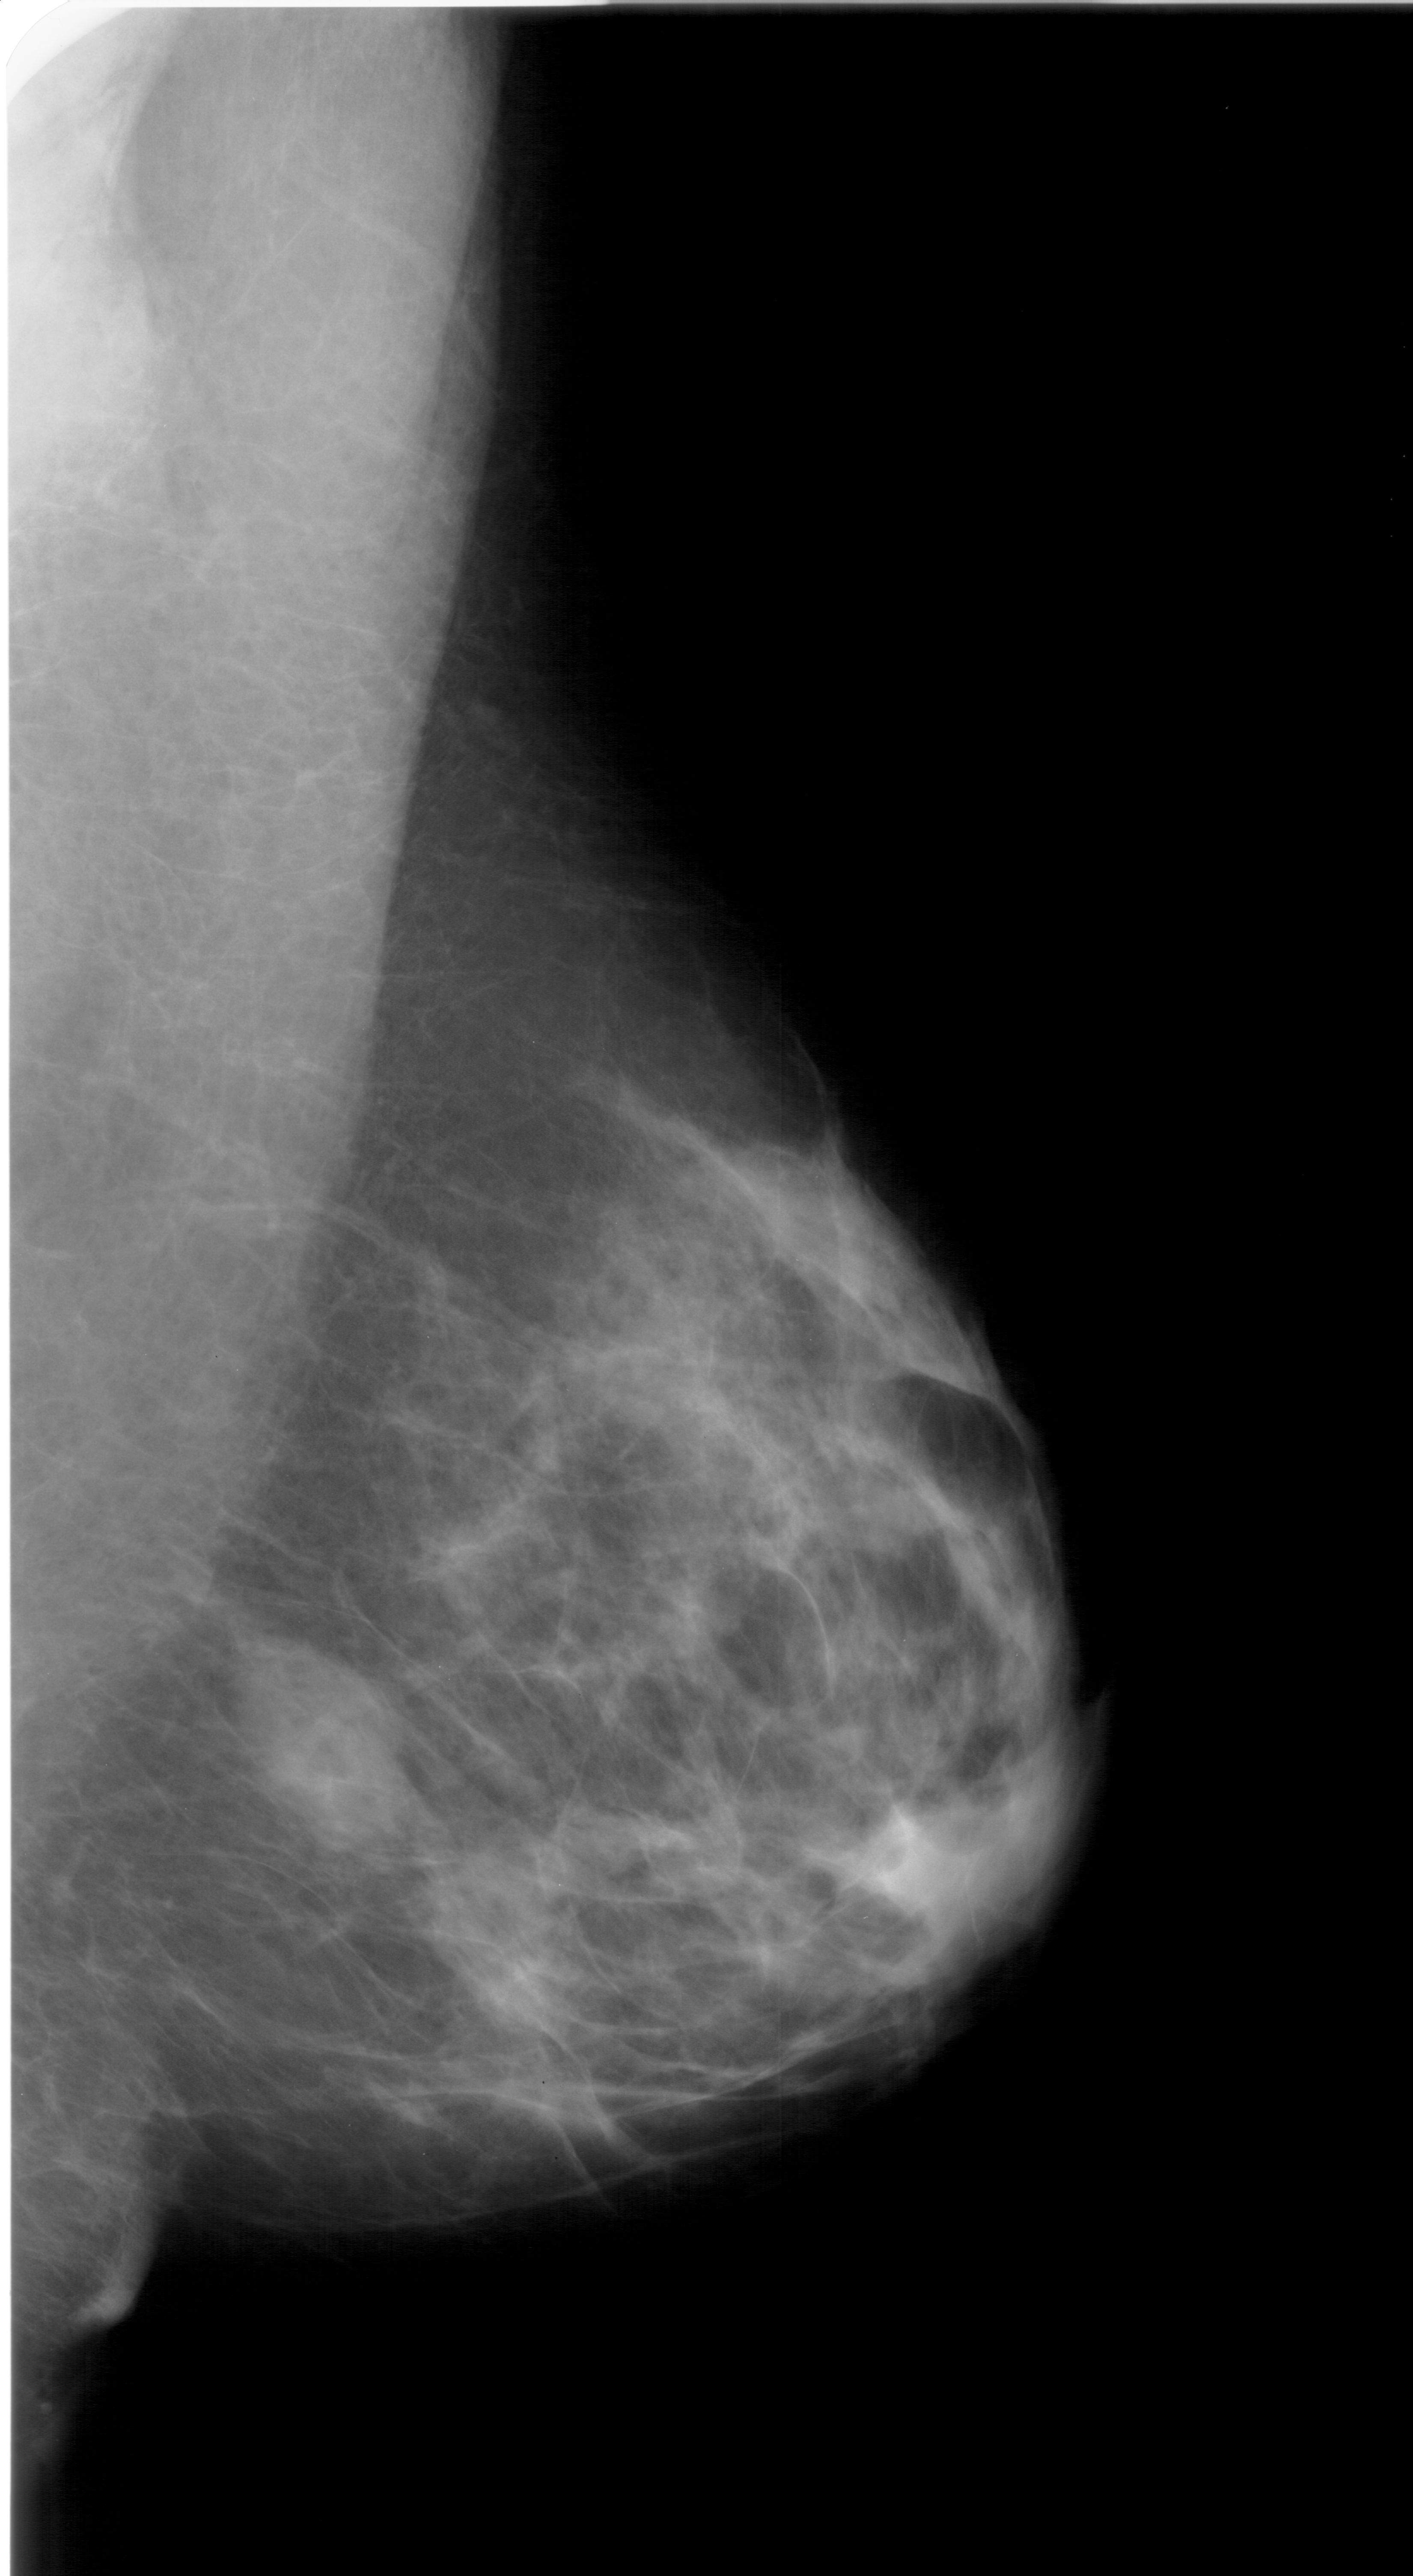
Mammogram (digitized film); right breast; MLO view; BI-RADS breast density category 2 (scale 1–4); 1413 × 2576 image matrix.
Expert-marked regions of interest on this image (one box per marked abnormality):
- mass, shape oval, margins ill defined; BI-RADS assessment category 4; subtlety rating 4 on a 1 (subtle) to 5 (obvious) scale; pathology (as recorded): benign: box from (x=227, y=1647) to (x=412, y=1860) px